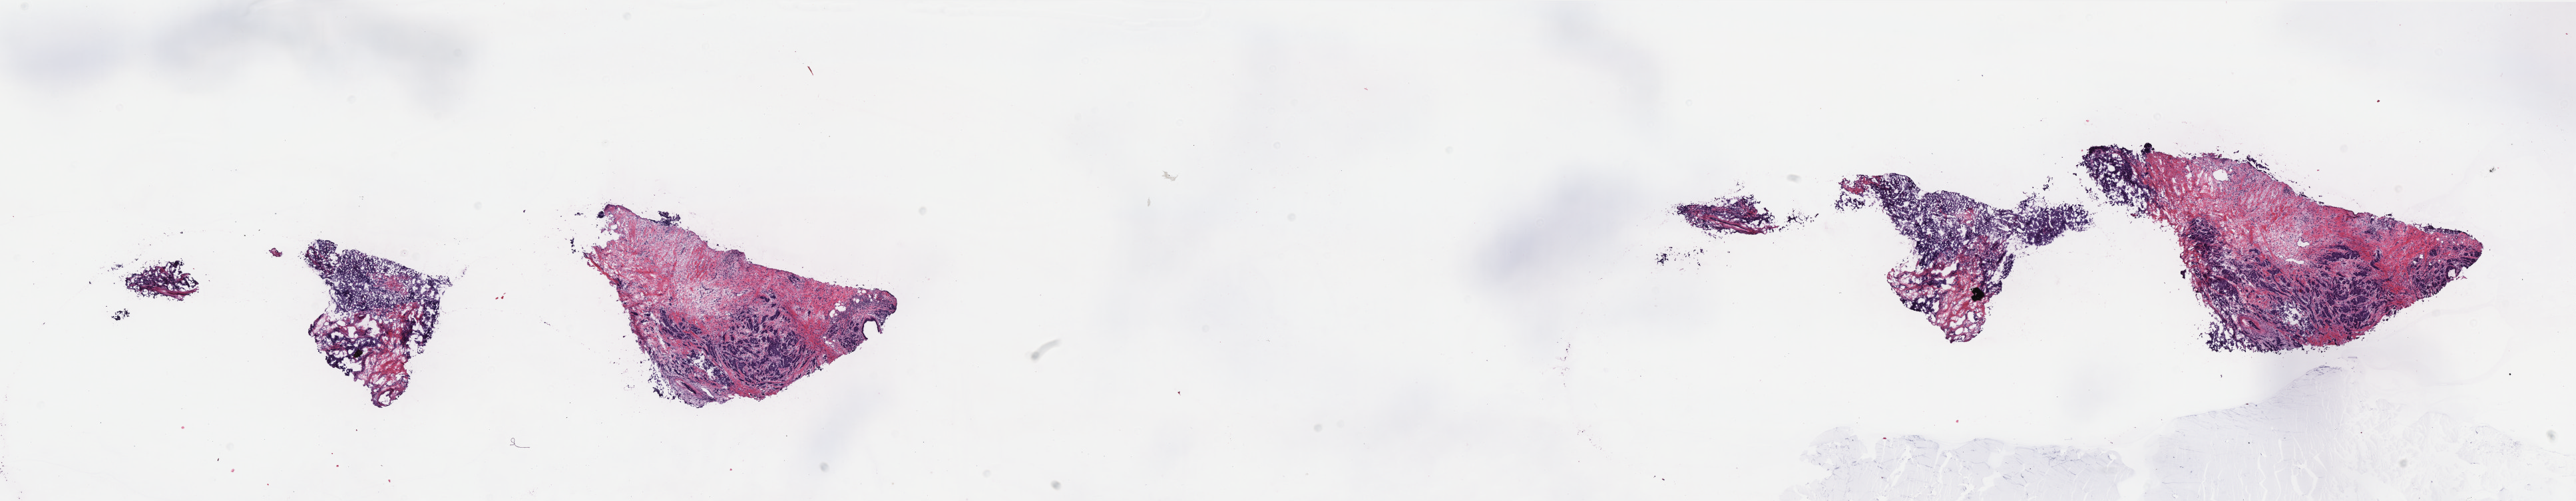
Digitized H&E tissue section (whole slide) — low-resolution overview of the scanned area, about 31.0 x 6.0 mm (acquisition: 40x scan); frozen section from the top of the tissue portion; breast, primary tumour sample. Female, age 67 years at initial diagnosis. Composition of this section per pathologist review: tumour cells 70%, tumour nuclei 70%, normal cells 3%, stromal cells 27%, necrosis 0%. Inflammatory infiltration, as recorded: lymphocyte infiltration 5%, monocyte infiltration 0%, neutrophil infiltration 0%.
AJCC pathologic stage: IIB. Lymph nodes positive (case pathology): 1 of 36 examined. Histologic diagnosis: Infiltrating duct mixed with other types of carcinoma. Laterality: right.